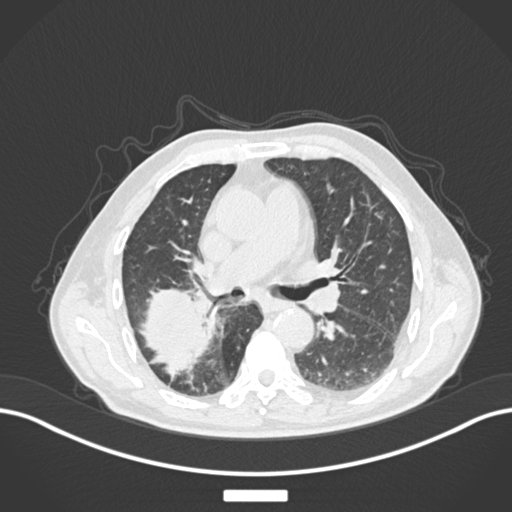
Chest CT, one axial slice; position 98 of 201 along the scan axis; lung window (W 1500 / L -600 HU); 512 × 512 image matrix, field of view 400 × 400 mm. Patient: male, 72 years. From the clinical record (not read from this slice): clinical TNM (as recorded): T3 N2 M0.
Structures marked on this image (rectangle marked by the reading radiologist):
- lung tumour (recorded histology: adenocarcinoma): bounding box [x1, y1, x2, y2] px = [139, 285, 215, 378]